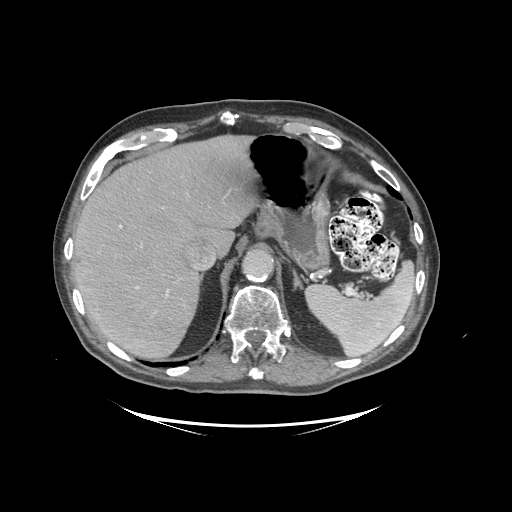
Contrast-enhanced abdominal CT (liver protocol), one axial slice. Slice 73 of 99 in the series (ordered by position). 140 kVp. Soft-tissue window (W 400 / L 40 HU). 2.5 mm slice thickness. 512 × 512 image matrix. From the clinical record (not read from this slice): diagnosis: hepatocellular carcinoma (patient treated with transarterial chemoembolisation; whether this scan precedes or follows treatment is not stated here); TNM stage (as recorded): Stage-I; Child-Pugh class: A; tumour differentiation: moderately differentiated.
Annotated regions visible in this slice (semi-automatic segmentation, software-assisted and operator-edited):
- liver parenchyma outside the tumour (the mass and vessels are separate outlines, so this box may not span the whole liver): bounding box [x1, y1, x2, y2] px = [72, 134, 256, 358]
- liver vessels: [119, 225, 169, 293]